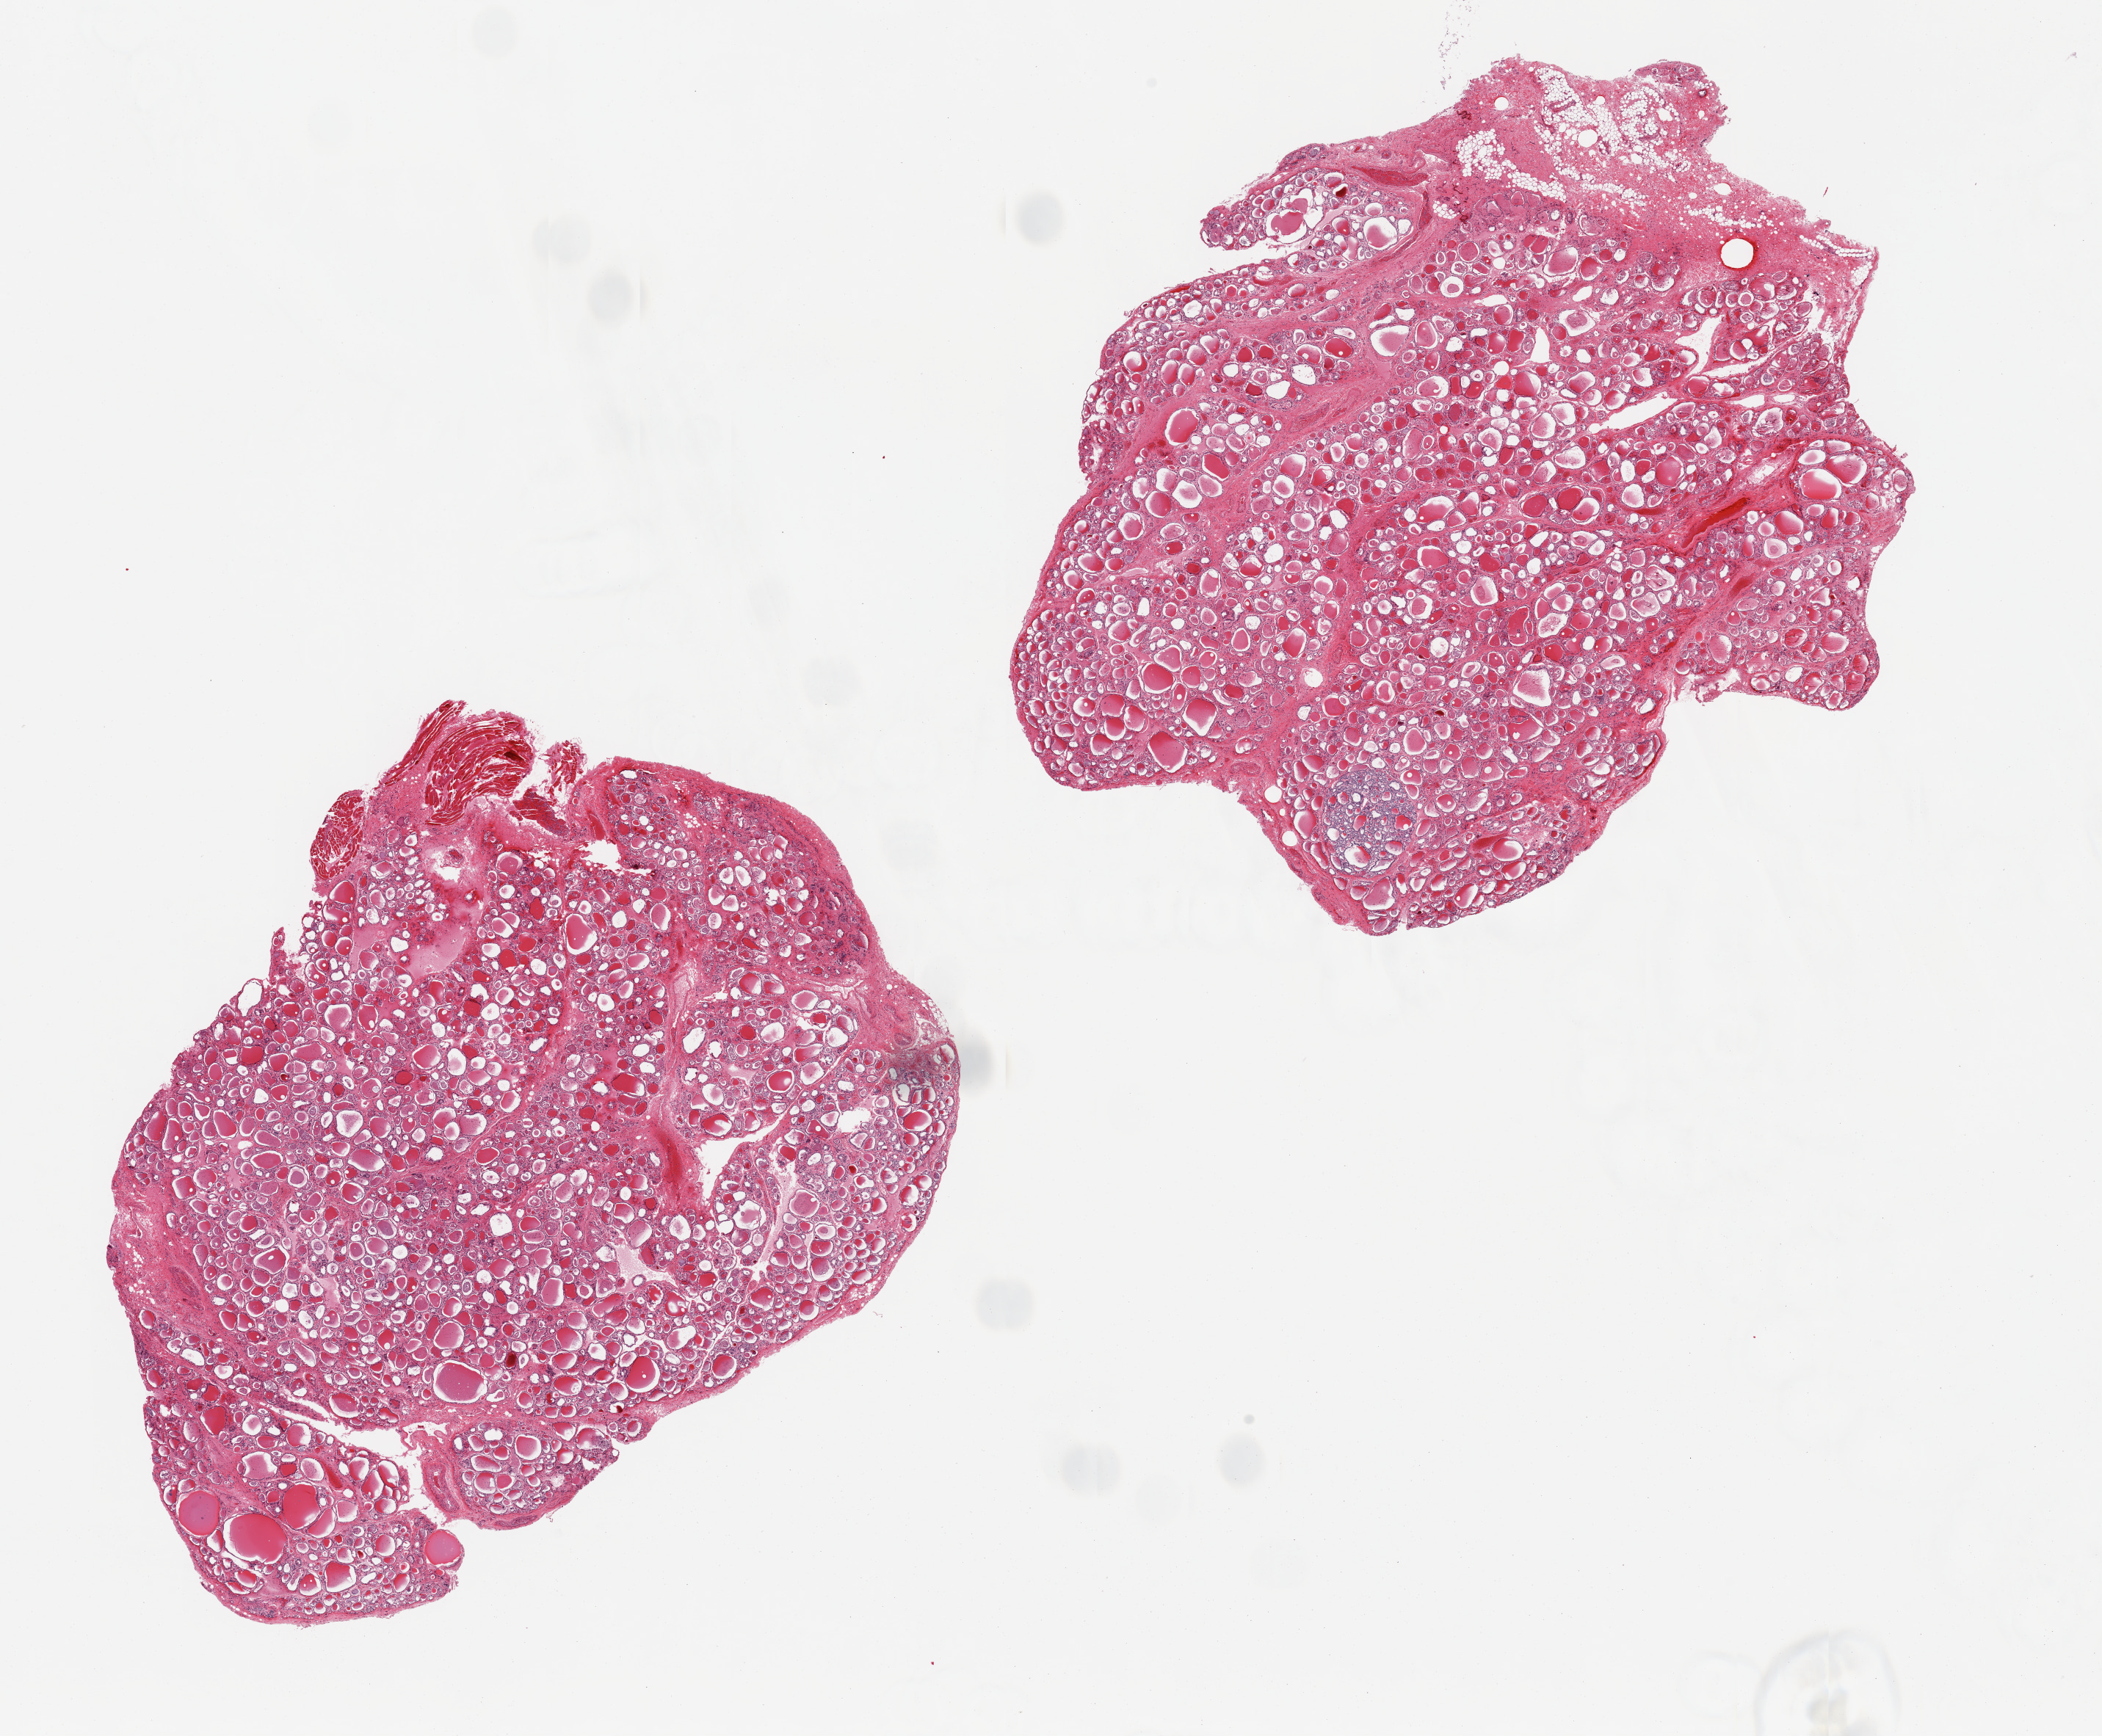
Whole-slide image, H&E stain — low-resolution overview of the scanned area, about 22.6 x 18.7 mm (from a 20x scan). PAXgene-fixed, paraffin-embedded tissue. Target tissue: thyroid. Donor tissue sample. Donor: male.
Reviewer comment on this tissue sample: 2 pieces; 1 mm adenomatoid nodule.